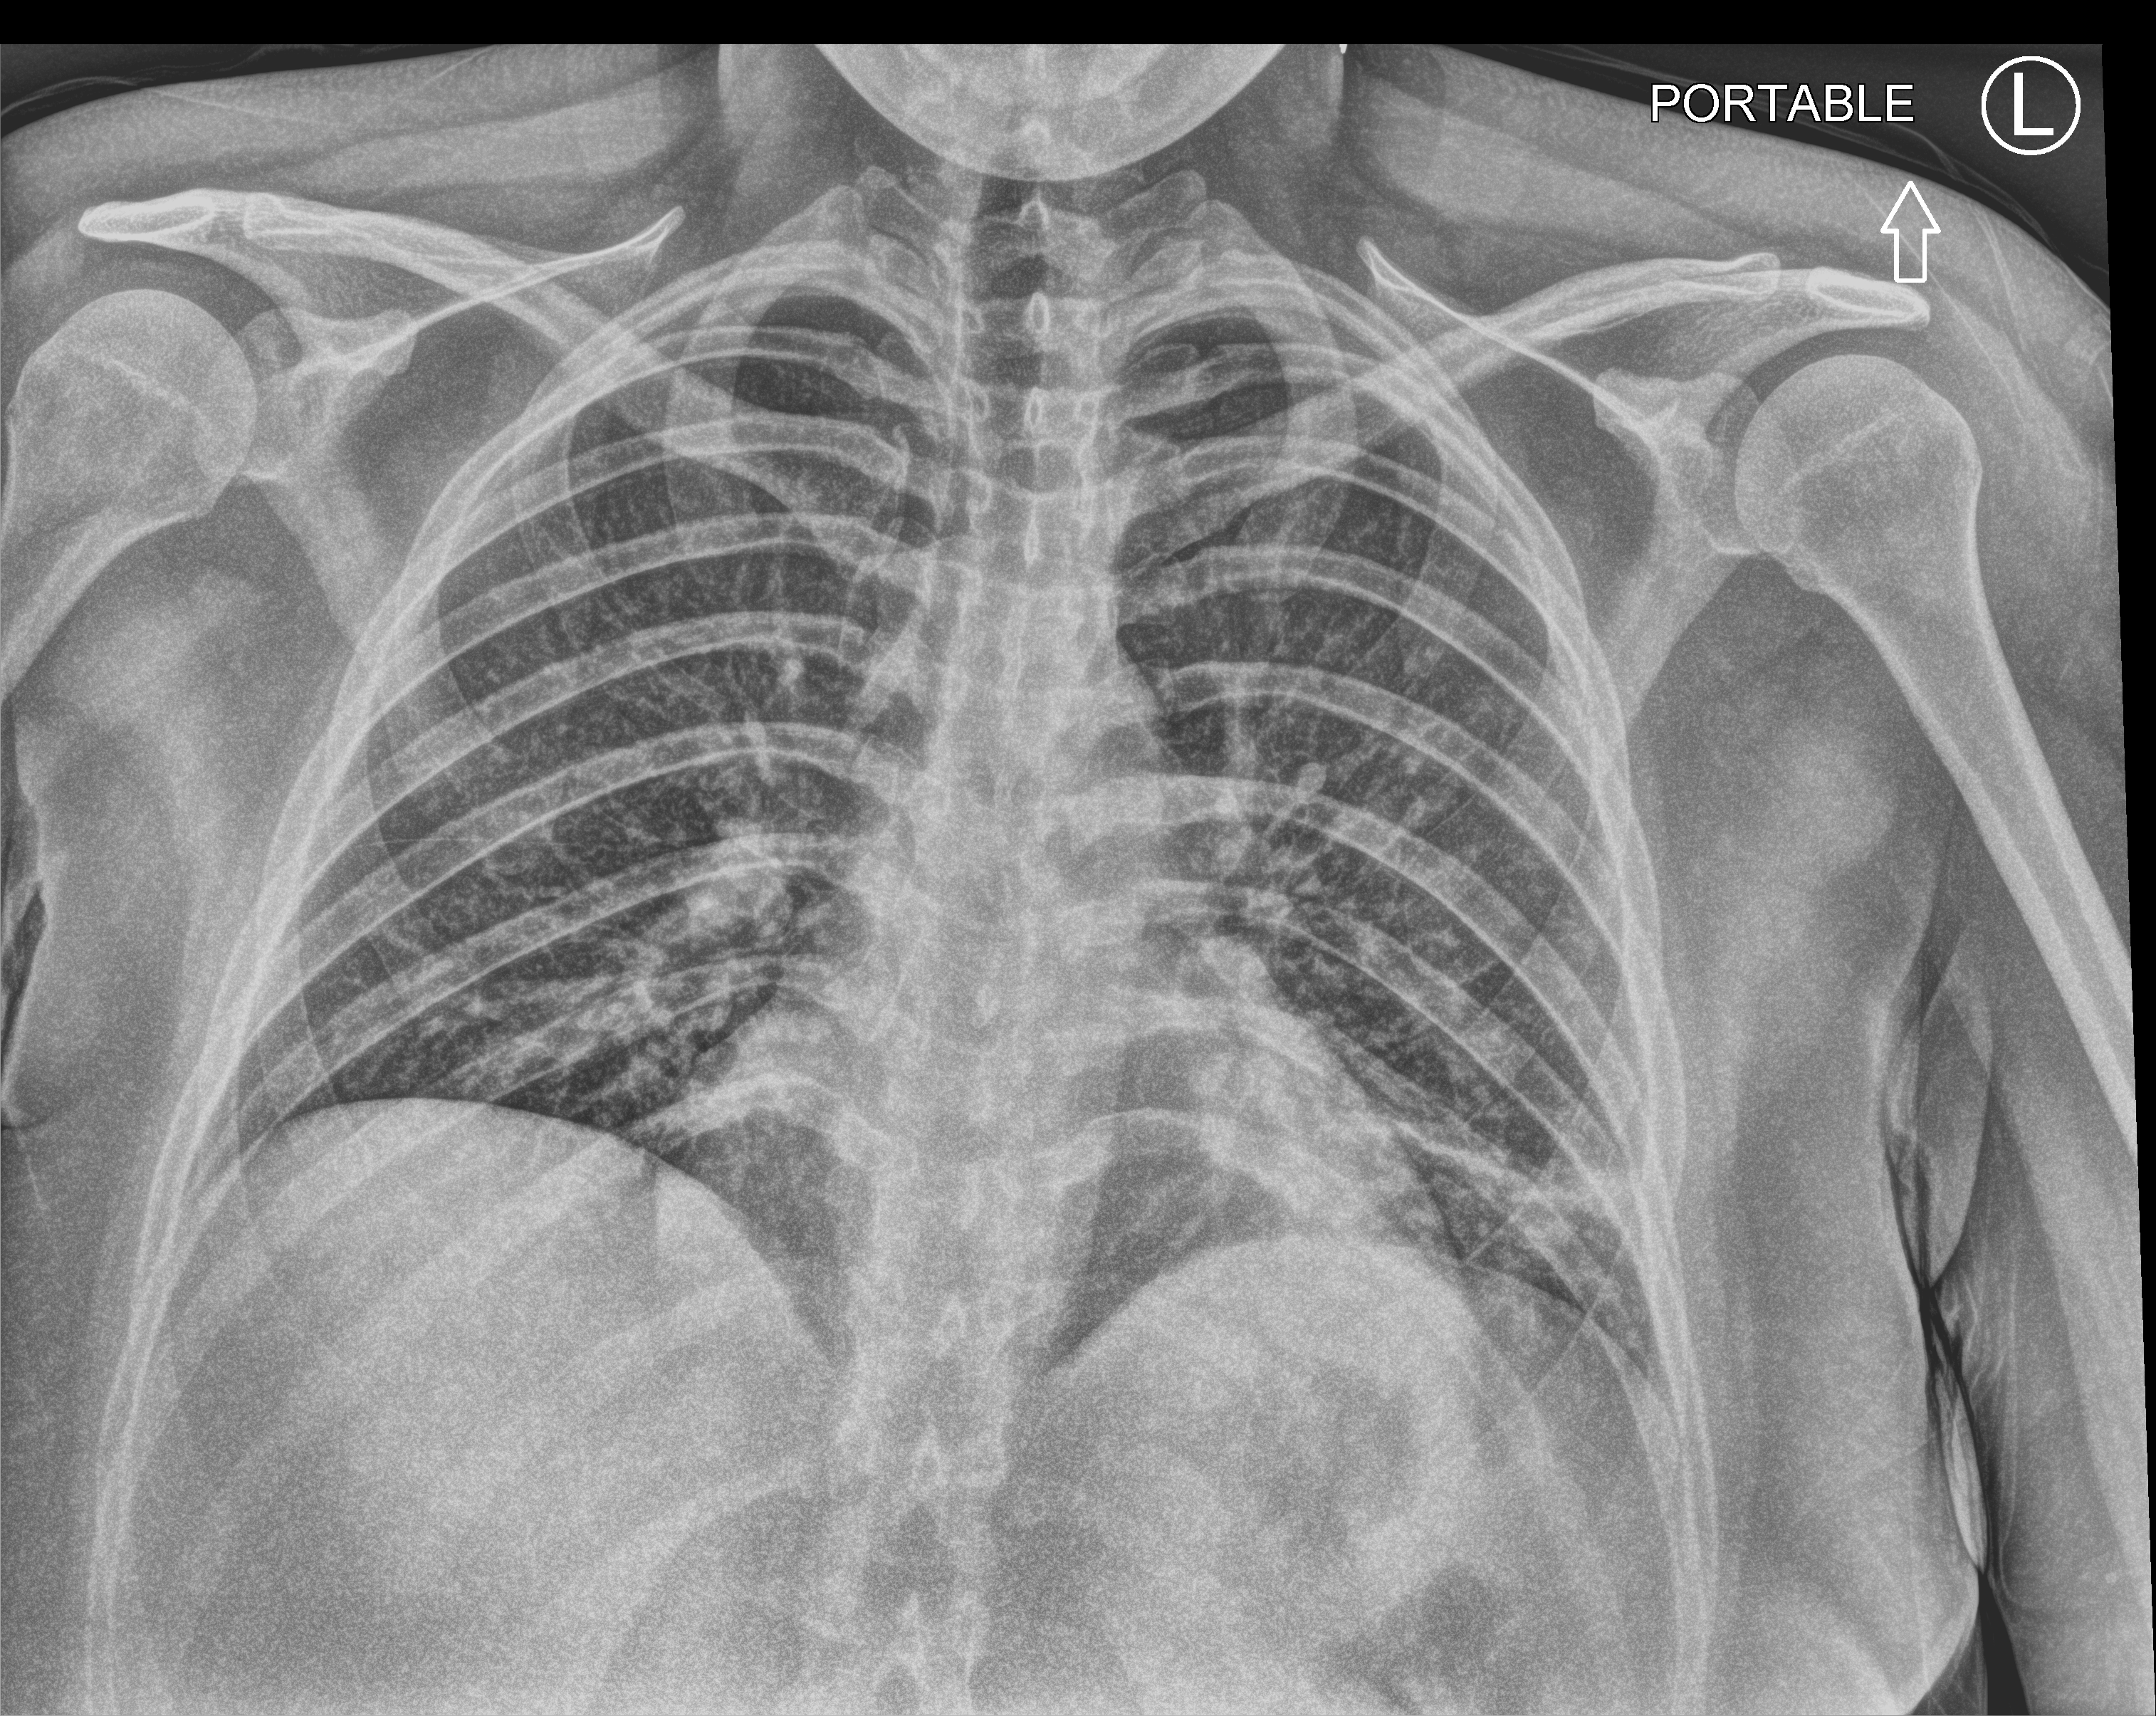
Bedside chest radiograph (computed radiography); anteroposterior (AP) projection. Patient hospitalised with COVID-19; female, aged 18–59 years.
From the hospital-stay record, not from the radiograph (when in the stay this image was taken is not recorded): other chronic lung disease (admission record): no.